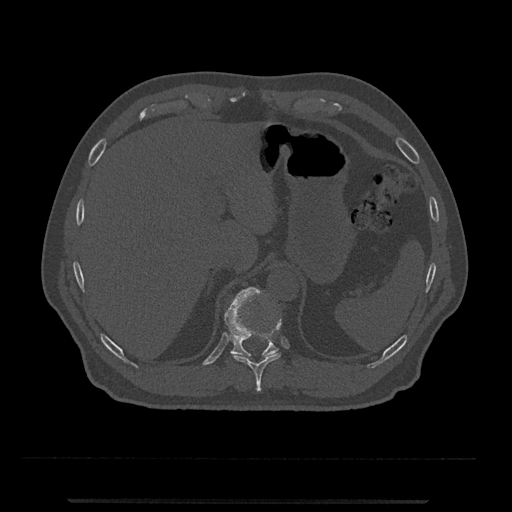
CT including the spine, one axial slice. Slice 493 of 797 in the series (ordered by position). Reconstruction kernel Br40s/3. 120 kVp. Bone window (W 1800 / L 400 HU). 0.5 mm slice thickness. 512 × 512 image matrix, field of view 419 × 419 mm. Patient: male, 63 years. From the clinical record (not read from this slice): primary cancer: prostate.
Structures marked on this image (semi-automatically segmented with operator editing):
- T10 vertebra: bounding box <233,323,281,392> (left, top, right, bottom; pixels)
- T11 vertebra: <224,287,279,357>